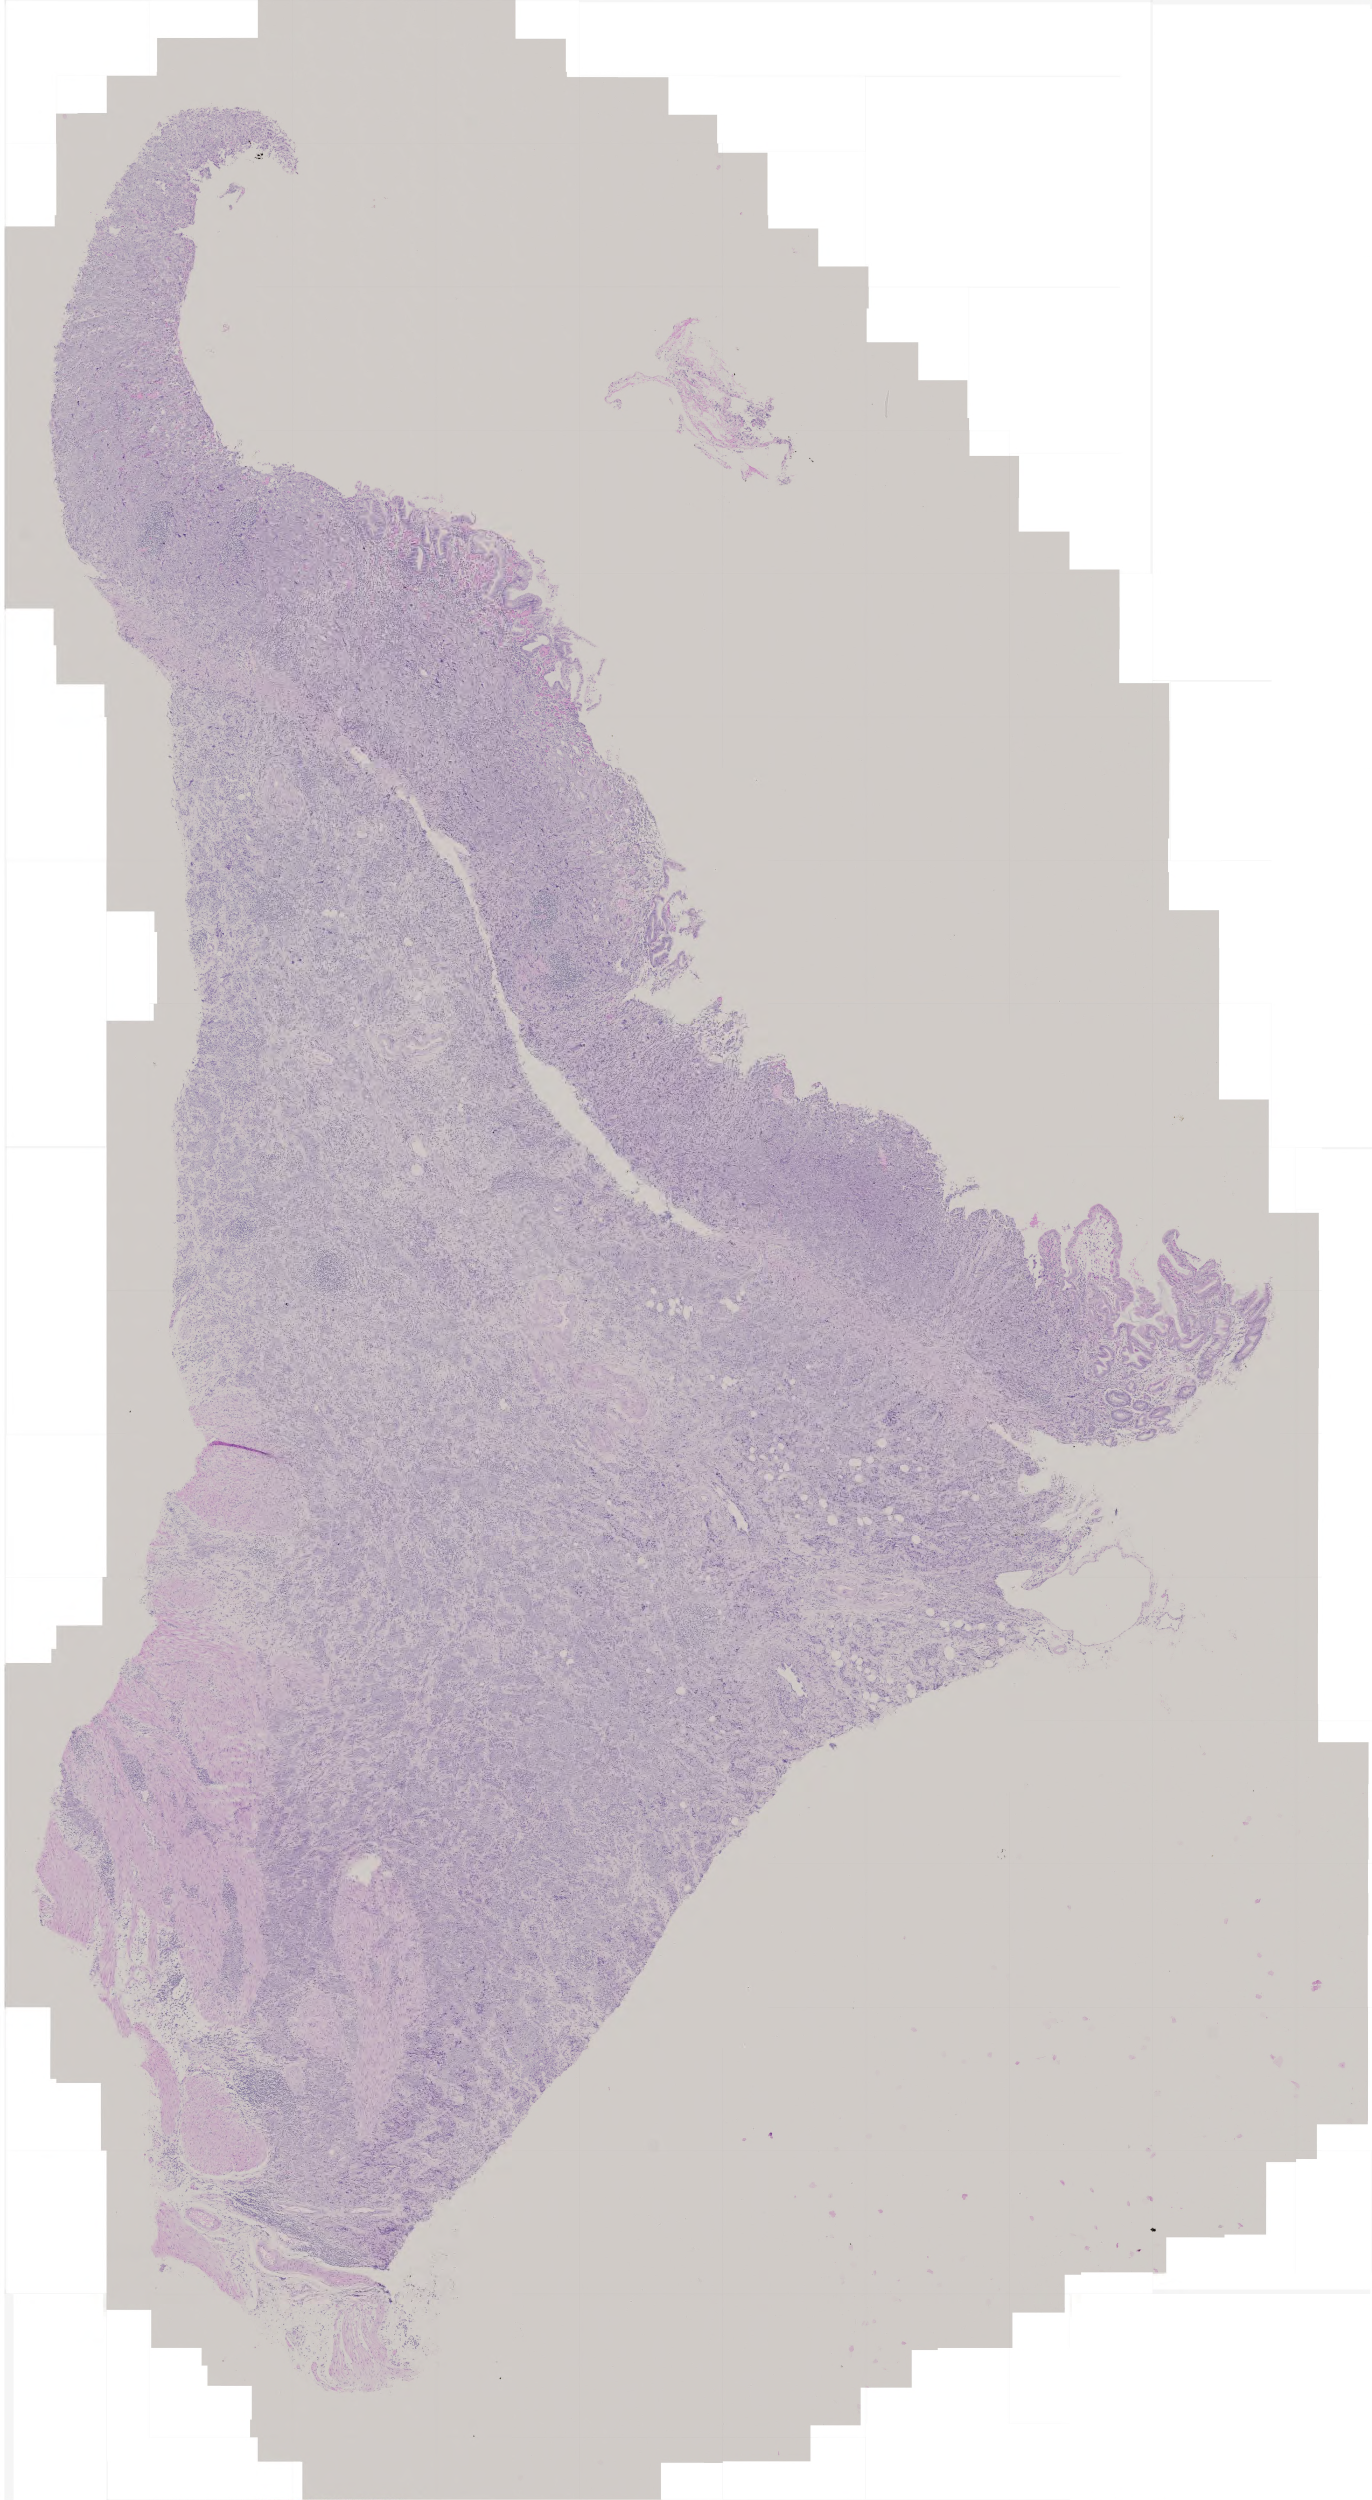
Whole-slide histology image, H&E — shown as a low-resolution overview of the whole scanned area (about 2.7 x 5.0 mm); FFPE section; sample: primary tumour, stomach. Female patient; age at initial diagnosis 67 years. Histologic grade: G3 (poorly differentiated).
Lymph nodes positive (case pathology): 15 of 21 examined. AJCC pathologic stage: IV (5th edition). Pathologic diagnosis: Adenocarcinoma, intestinal type.